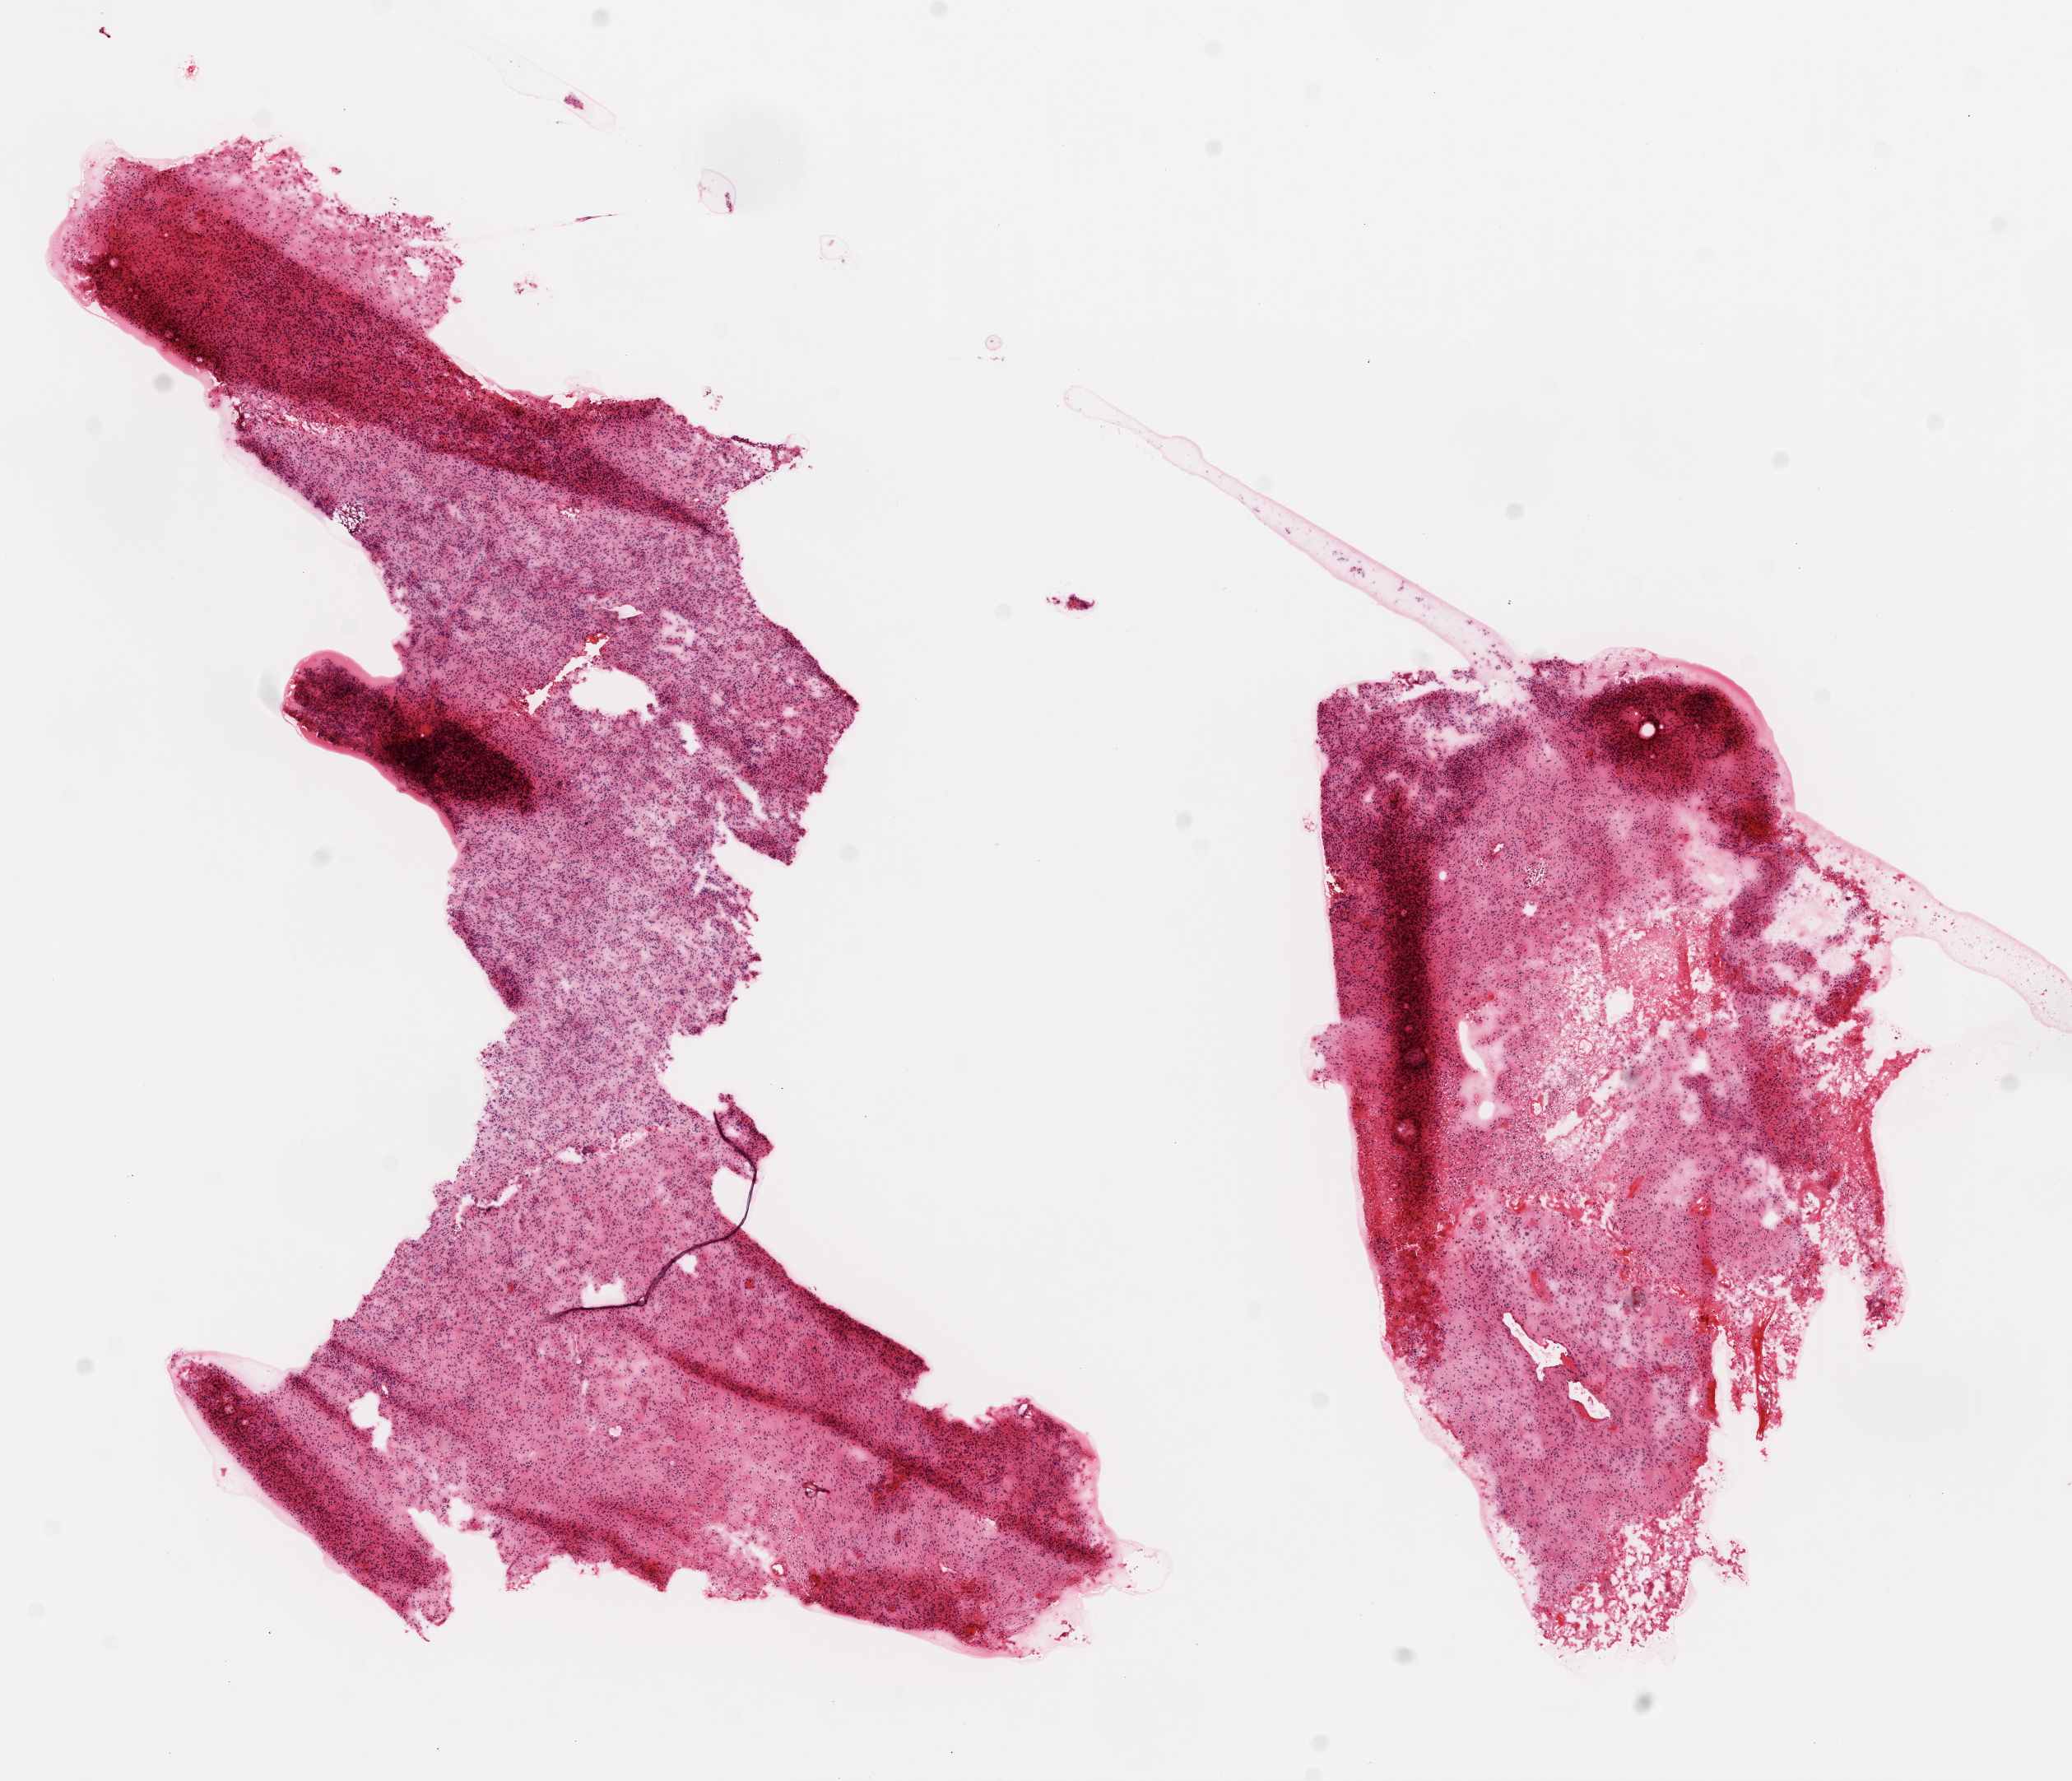
Whole-slide histology image, H&E-stained — low-resolution overview of the scanned area, about 10.2 x 8.7 mm (from a 20x scan); frozen section; brain, primary tumour sample. Female patient; age at initial diagnosis 57 years. Pathologist review of this section (percent, as recorded): tumour cells 80%, tumour nuclei 90%, normal cells 0%, stromal cells 10%, necrosis 10%.
• diagnosis: Glioblastoma